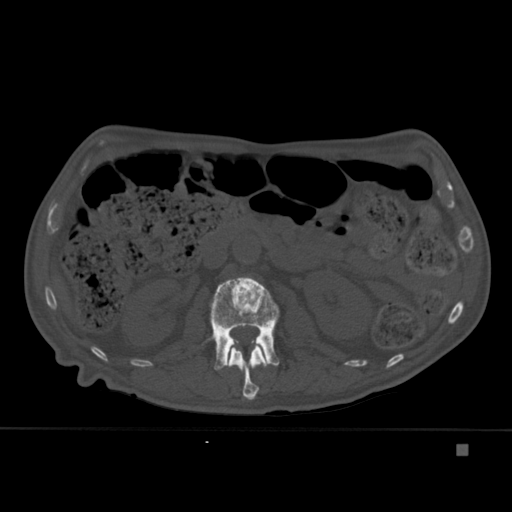
CT including the spine, one axial slice; slice 169 of 451 in the series (ordered by position); bone window (W 1800 / L 400 HU); 1.5 mm slice thickness; 512 × 512 image matrix, field of view 378 × 378 mm. Male patient, age 75 years. From the clinical record (not read from this slice): primary cancer: prostate.
Annotated regions visible in this slice (semi-automatic segmentation, software-assisted and operator-edited):
- L1 vertebra: bounding box <227,344,268,400> (left, top, right, bottom; pixels)
- L2 vertebra: <202,277,279,370>